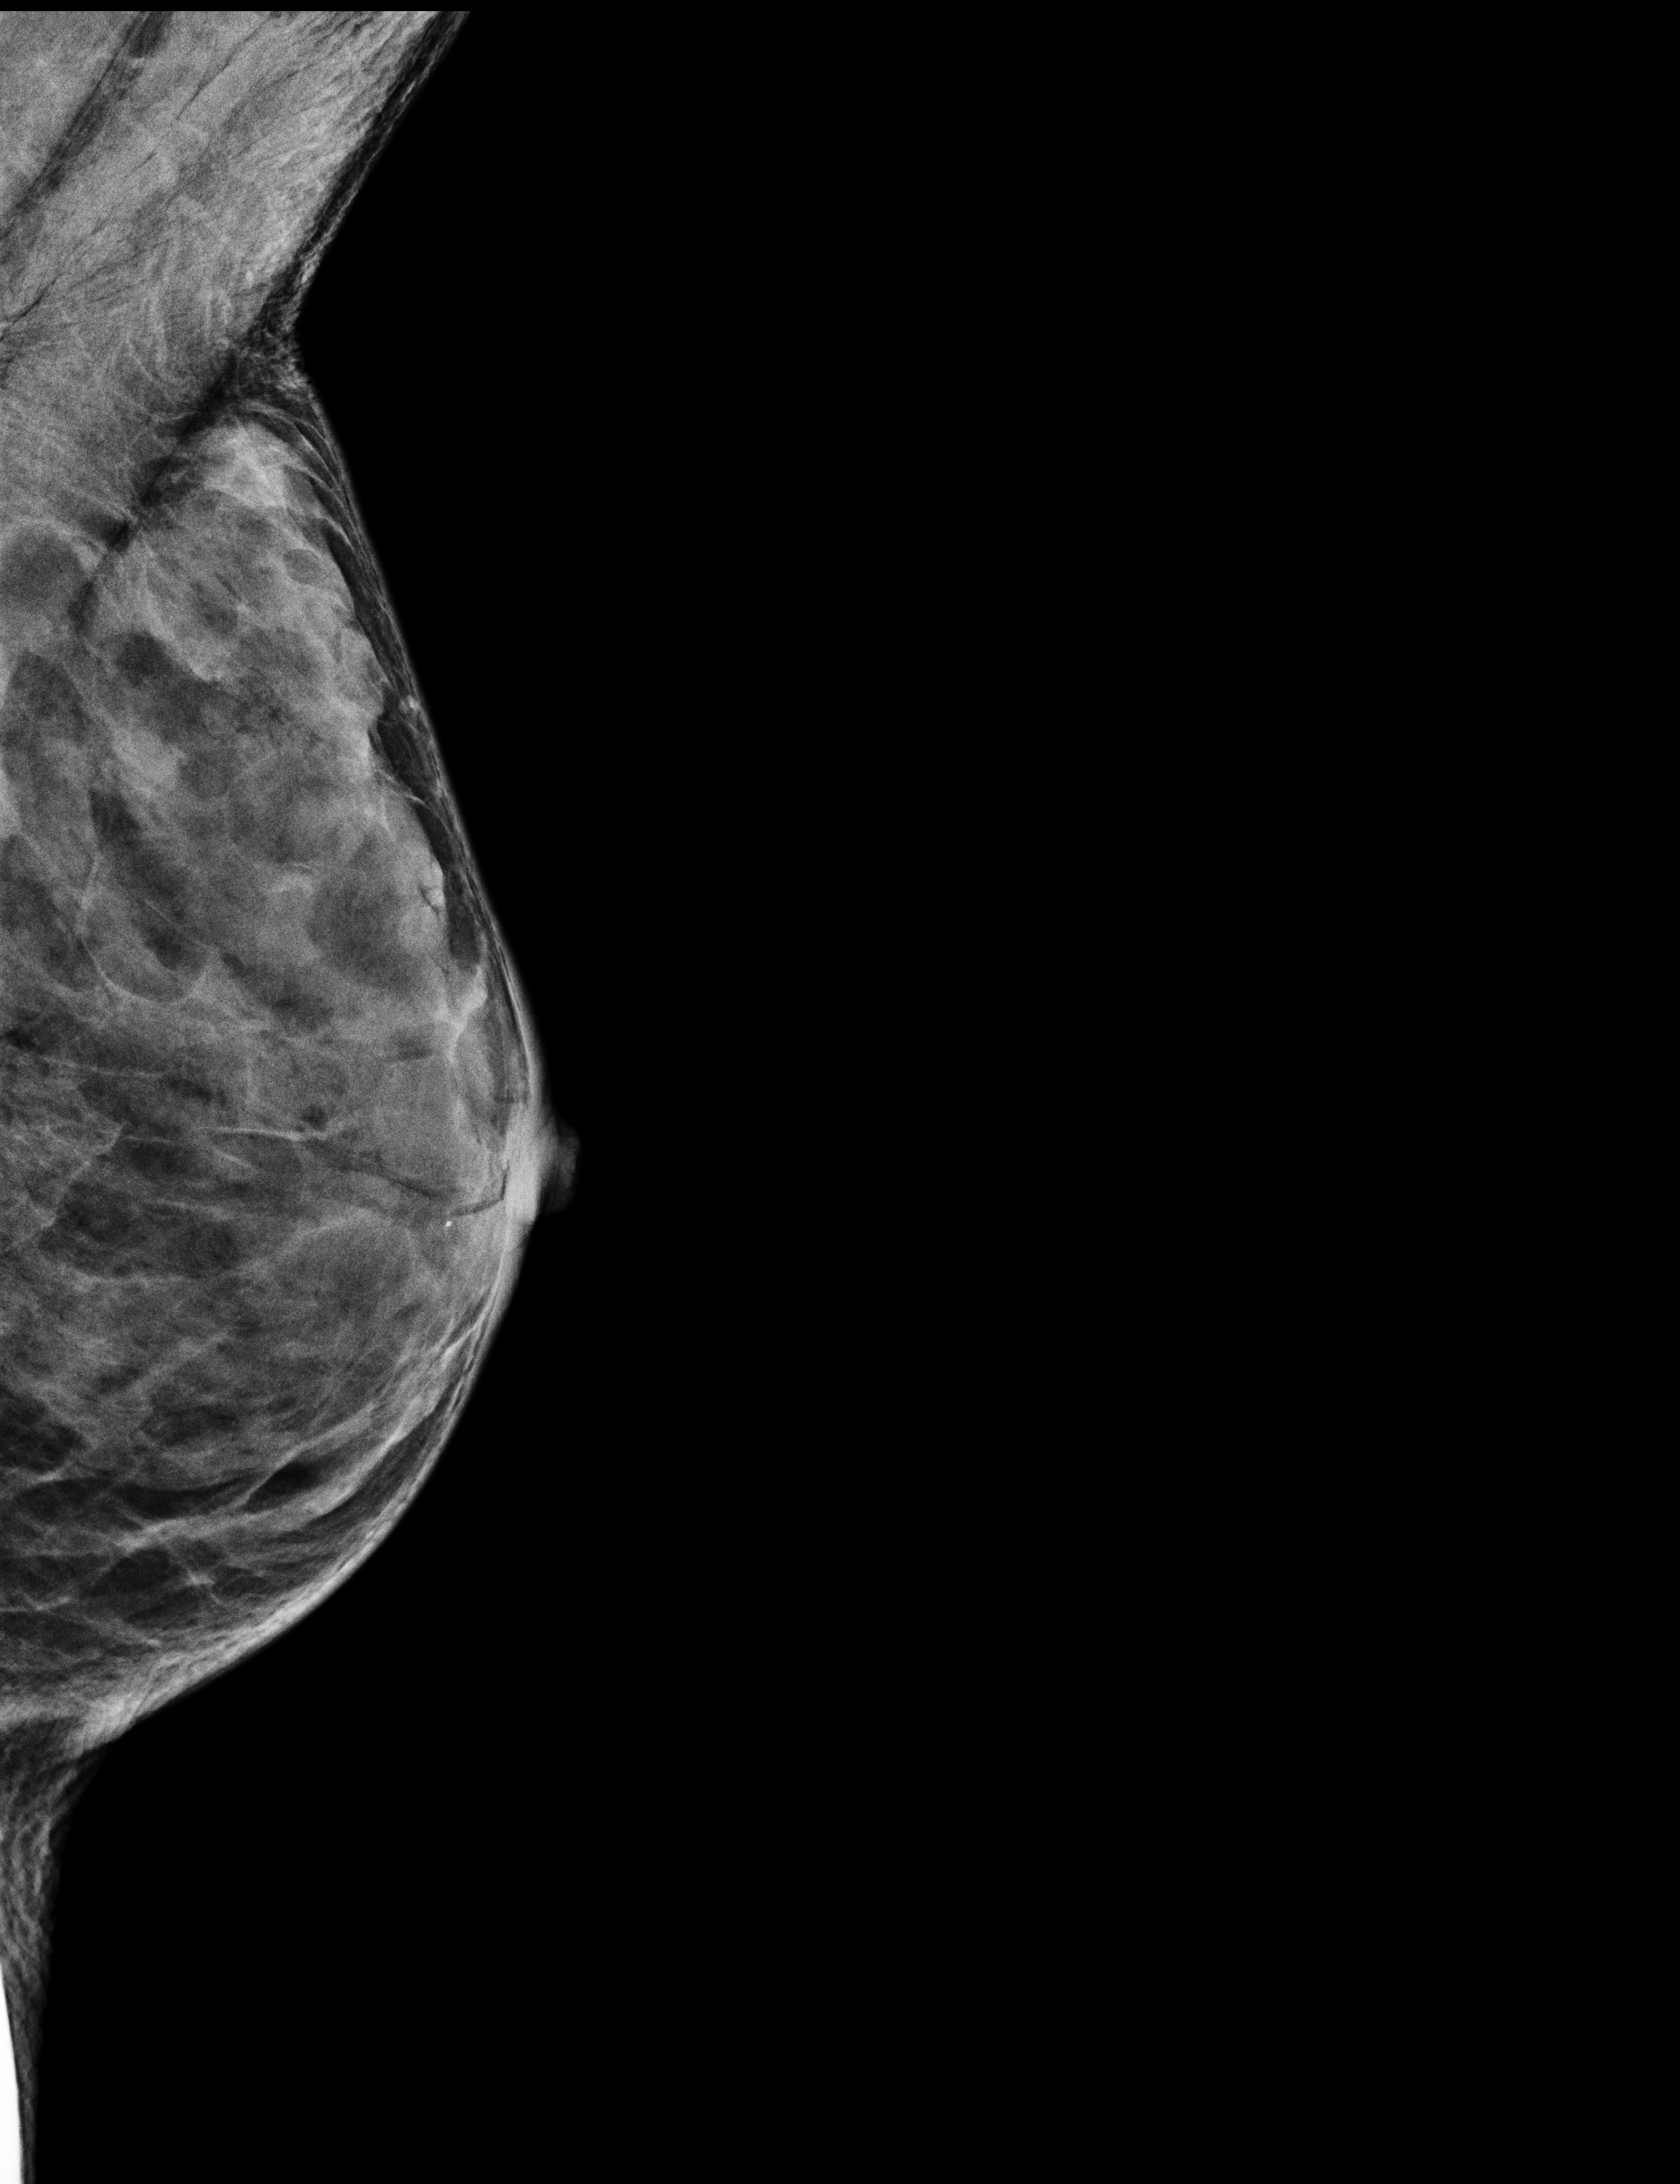
Annual screening mammography examination, compressed breast thickness 23 mm. Female patient, age 69 years.
Image type: full-field digital mammogram. Breast: left. Projection: MLO view.